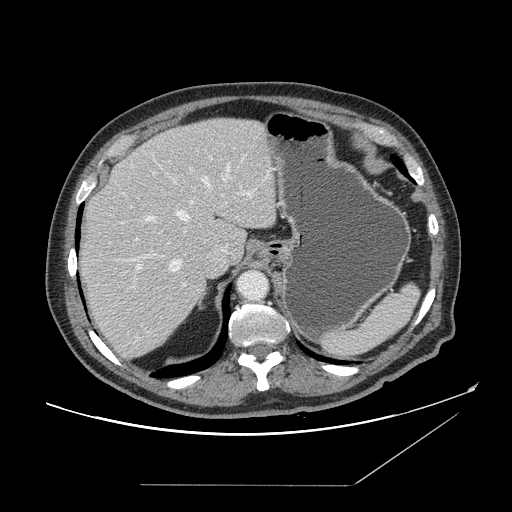
Contrast-enhanced abdominal CT, one axial slice; position 117 of 166 along the scan axis; intravenous contrast given; soft-tissue window (W 400 / L 40 HU); 512 × 512 image matrix. Male patient, age 80 years. From the clinical record (not read from this slice): diagnosis: colorectal cancer liver metastases, imaged before liver resection; multiple liver metastases: no; largest metastasis: 2.2 cm; disease in both lobes: no.
Outlined on this slice (outlined manually by an expert reader):
- hepatic veins: bounding box [x1, y1, x2, y2] px = [124, 164, 231, 272]
- liver: [79, 118, 276, 359]
- planned liver remnant (the part of the liver to remain after resection): [82, 118, 276, 263]
- portal vein (with intrahepatic branches): [136, 157, 251, 270]